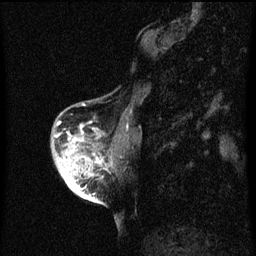
Breast MRI (dynamic contrast-enhanced), one sagittal slice; dynamic contrast-enhanced series, image 2 of 3 at this slice position (ordered by acquisition); 1.5 T; TE 4.2 ms, TR 8 ms; 2 mm slice thickness; 256 × 256 image matrix. Patient: female, 56 years.
Outlined on this slice (semi-automatic segmentation, software-assisted and operator-edited):
- analysis volume of interest (the breast-tissue region the enhancement analysis was run in; not a lesion): bounding box (x1, y1, x2, y2) in pixels: (54, 122, 115, 199)
- tumour enhancement mask (voxels above the 70 % enhancement threshold inside the analysis volume of interest): (60, 128, 102, 199)